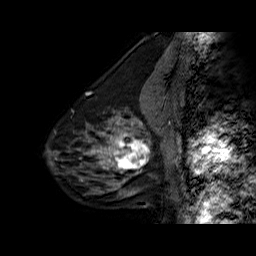
Breast MRI (dynamic contrast-enhanced), one sagittal slice; position 21 of 60 along the scan axis; dynamic contrast-enhanced series, time point 2 of 6 at this slice position (early post-contrast); 1.5 T; TE 6.3 ms, TR 32.5 ms; 4 mm slice thickness; 256 × 256 image matrix. Female patient. Case-level facts recorded for this patient, not image findings: setting: breast cancer imaged before/during neoadjuvant chemotherapy; receptor status: triple-negative.
Structures marked on this image (semi-automatically segmented with operator editing):
- analysis volume of interest (the breast-tissue region the enhancement analysis was run in; not a lesion): box from (x=108, y=126) to (x=154, y=177) px
- tumour enhancement mask (voxels above the 100 % enhancement threshold inside the analysis volume of interest): (x=108, y=132)–(x=150, y=174)